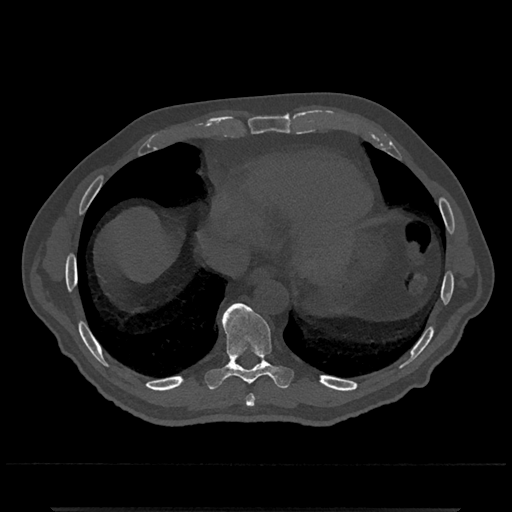
CT including the spine, one axial slice. Slice 613 of 797 in the series (ordered by position). Reconstruction kernel Br40s/3. Bone window (W 1800 / L 400 HU). 512 × 512 image matrix, field of view 393 × 393 mm. Male patient, age 67 years. From the clinical record (not read from this slice): primary cancer: prostate.
Outlined on this slice (semi-automatic segmentation, software-assisted and operator-edited):
- T8 vertebra: bounding box (x1, y1, x2, y2) in pixels: (246, 394, 255, 407)
- T9 vertebra: (205, 303, 294, 389)